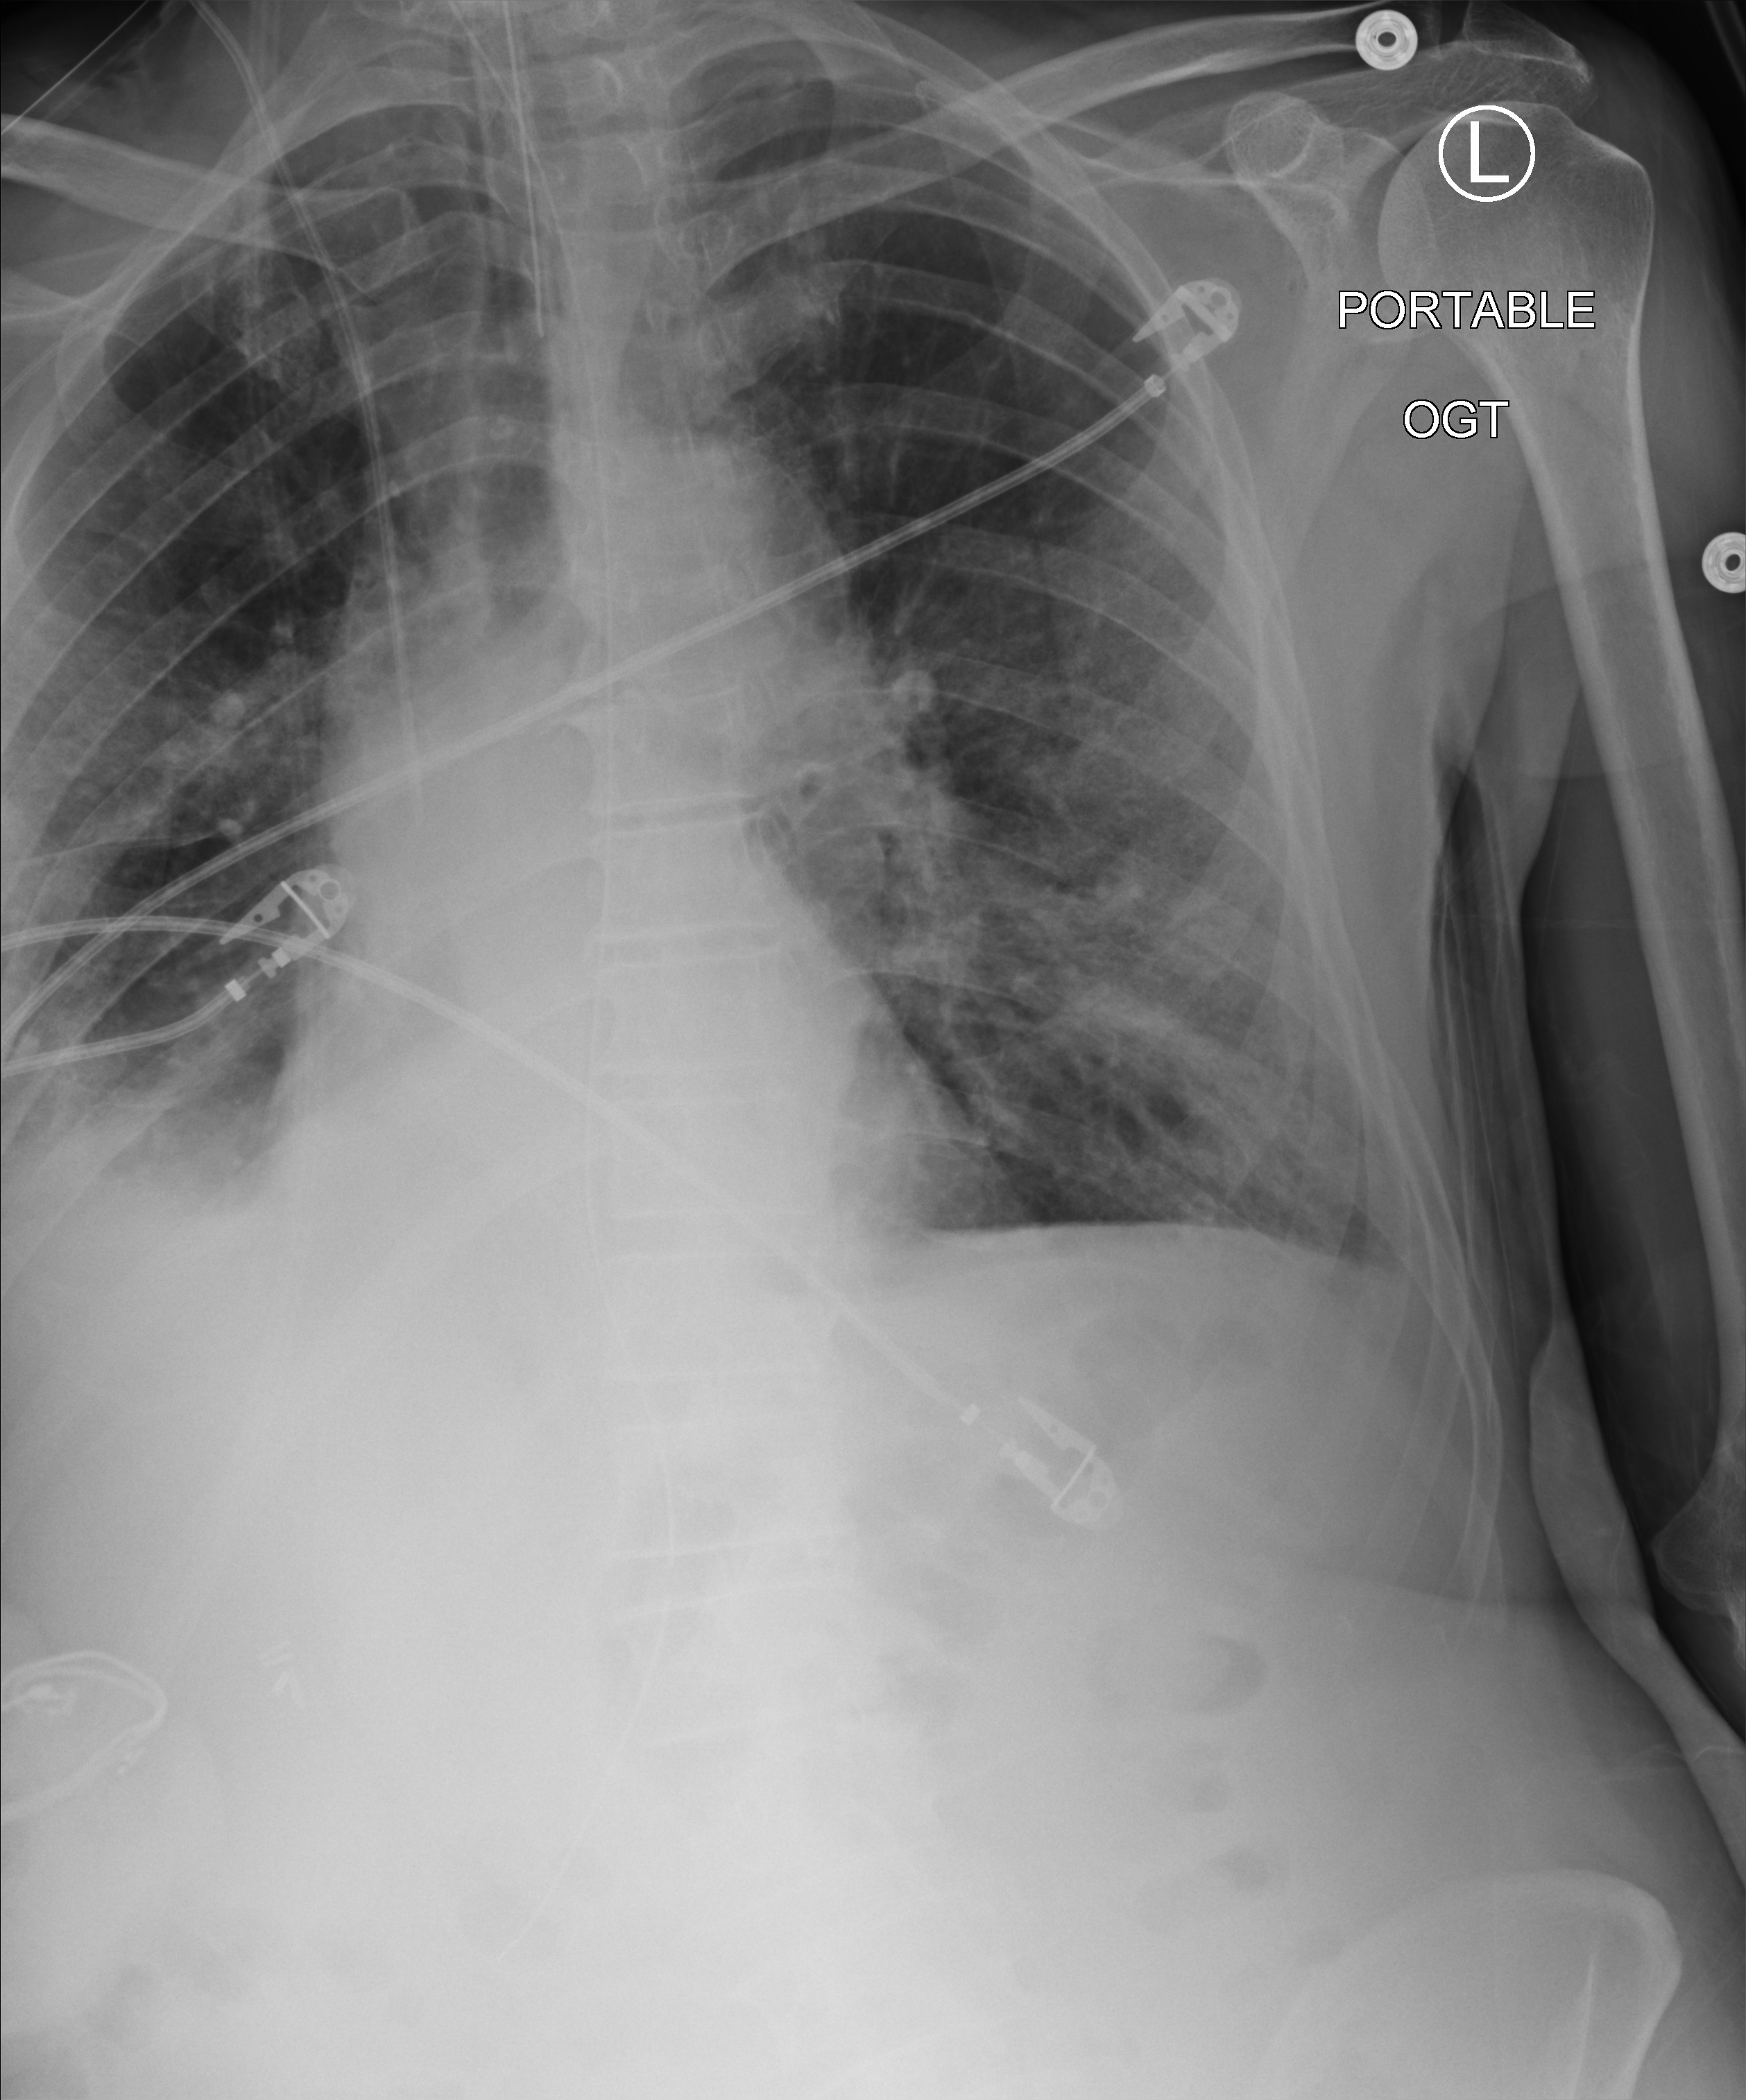
Chest X-ray (portable), anteroposterior (AP) projection. Patient hospitalised with COVID-19; male, aged 75–90 years.
Admission-level facts for this patient (not findings on this image; timing relative to this image not recorded): chronic kidney disease (admission record): no; admitted to intensive care during this hospital stay: yes.